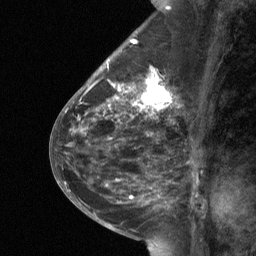
Breast MRI (dynamic contrast-enhanced), one sagittal slice; slice 26 of 64 in the series (ordered by position); dynamic contrast-enhanced study with each time point stored as its own series, time point 2 of 3 at this slice position (early post-contrast, ordered by acquisition time); 1.5 T; TE 4.8 ms, TR 27 ms; 2 mm slice thickness; 256 × 256 image matrix, field of view 180 × 180 mm. Female patient, age 59 years. From the clinical record (not read from this slice): setting: breast cancer imaged before/during neoadjuvant chemotherapy; receptor status: triple-negative.
Annotated regions visible in this slice (semi-automatically segmented with operator editing):
- analysis volume of interest (the breast-tissue region the enhancement analysis was run in; not a lesion): bounding box (x1, y1, x2, y2) in pixels: (113, 67, 175, 120)
- tumour enhancement mask (voxels above the 90 % enhancement threshold inside the analysis volume of interest): (113, 67, 172, 115)